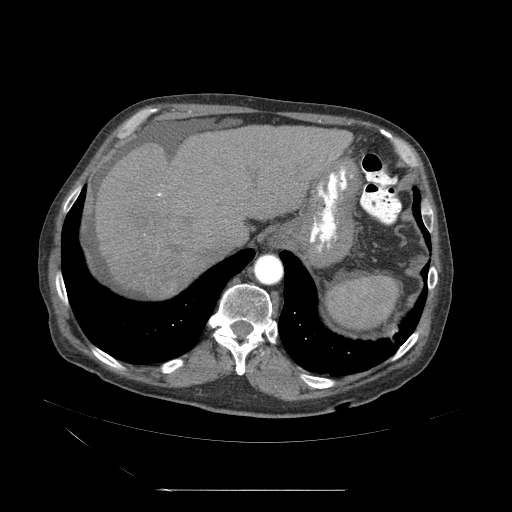
Contrast-enhanced abdominal CT (liver protocol), one axial slice; position 44 of 71 along the scan axis; 120 kVp; soft-tissue window (W 400 / L 40 HU); 2.5 mm slice thickness; 512 × 512 image matrix, field of view 440 × 440 mm. From the clinical record (not read from this slice): diagnosis: hepatocellular carcinoma (patient treated with transarterial chemoembolisation; whether this scan precedes or follows treatment is not stated here); TNM stage (as recorded): Stage-II; Child-Pugh class: A; tumour nodularity: multinodular; tumour size: 1 cm.
Structures marked on this image (semi-automatically segmented with operator editing):
- abdominal aorta: bounding box (x1, y1, x2, y2) in pixels: (254, 255, 284, 286)
- liver parenchyma outside the tumour (the mass and vessels are separate outlines, so this box may not span the whole liver): (86, 127, 355, 304)
- mass: (144, 263, 189, 305)
- liver vessels: (111, 198, 231, 266)